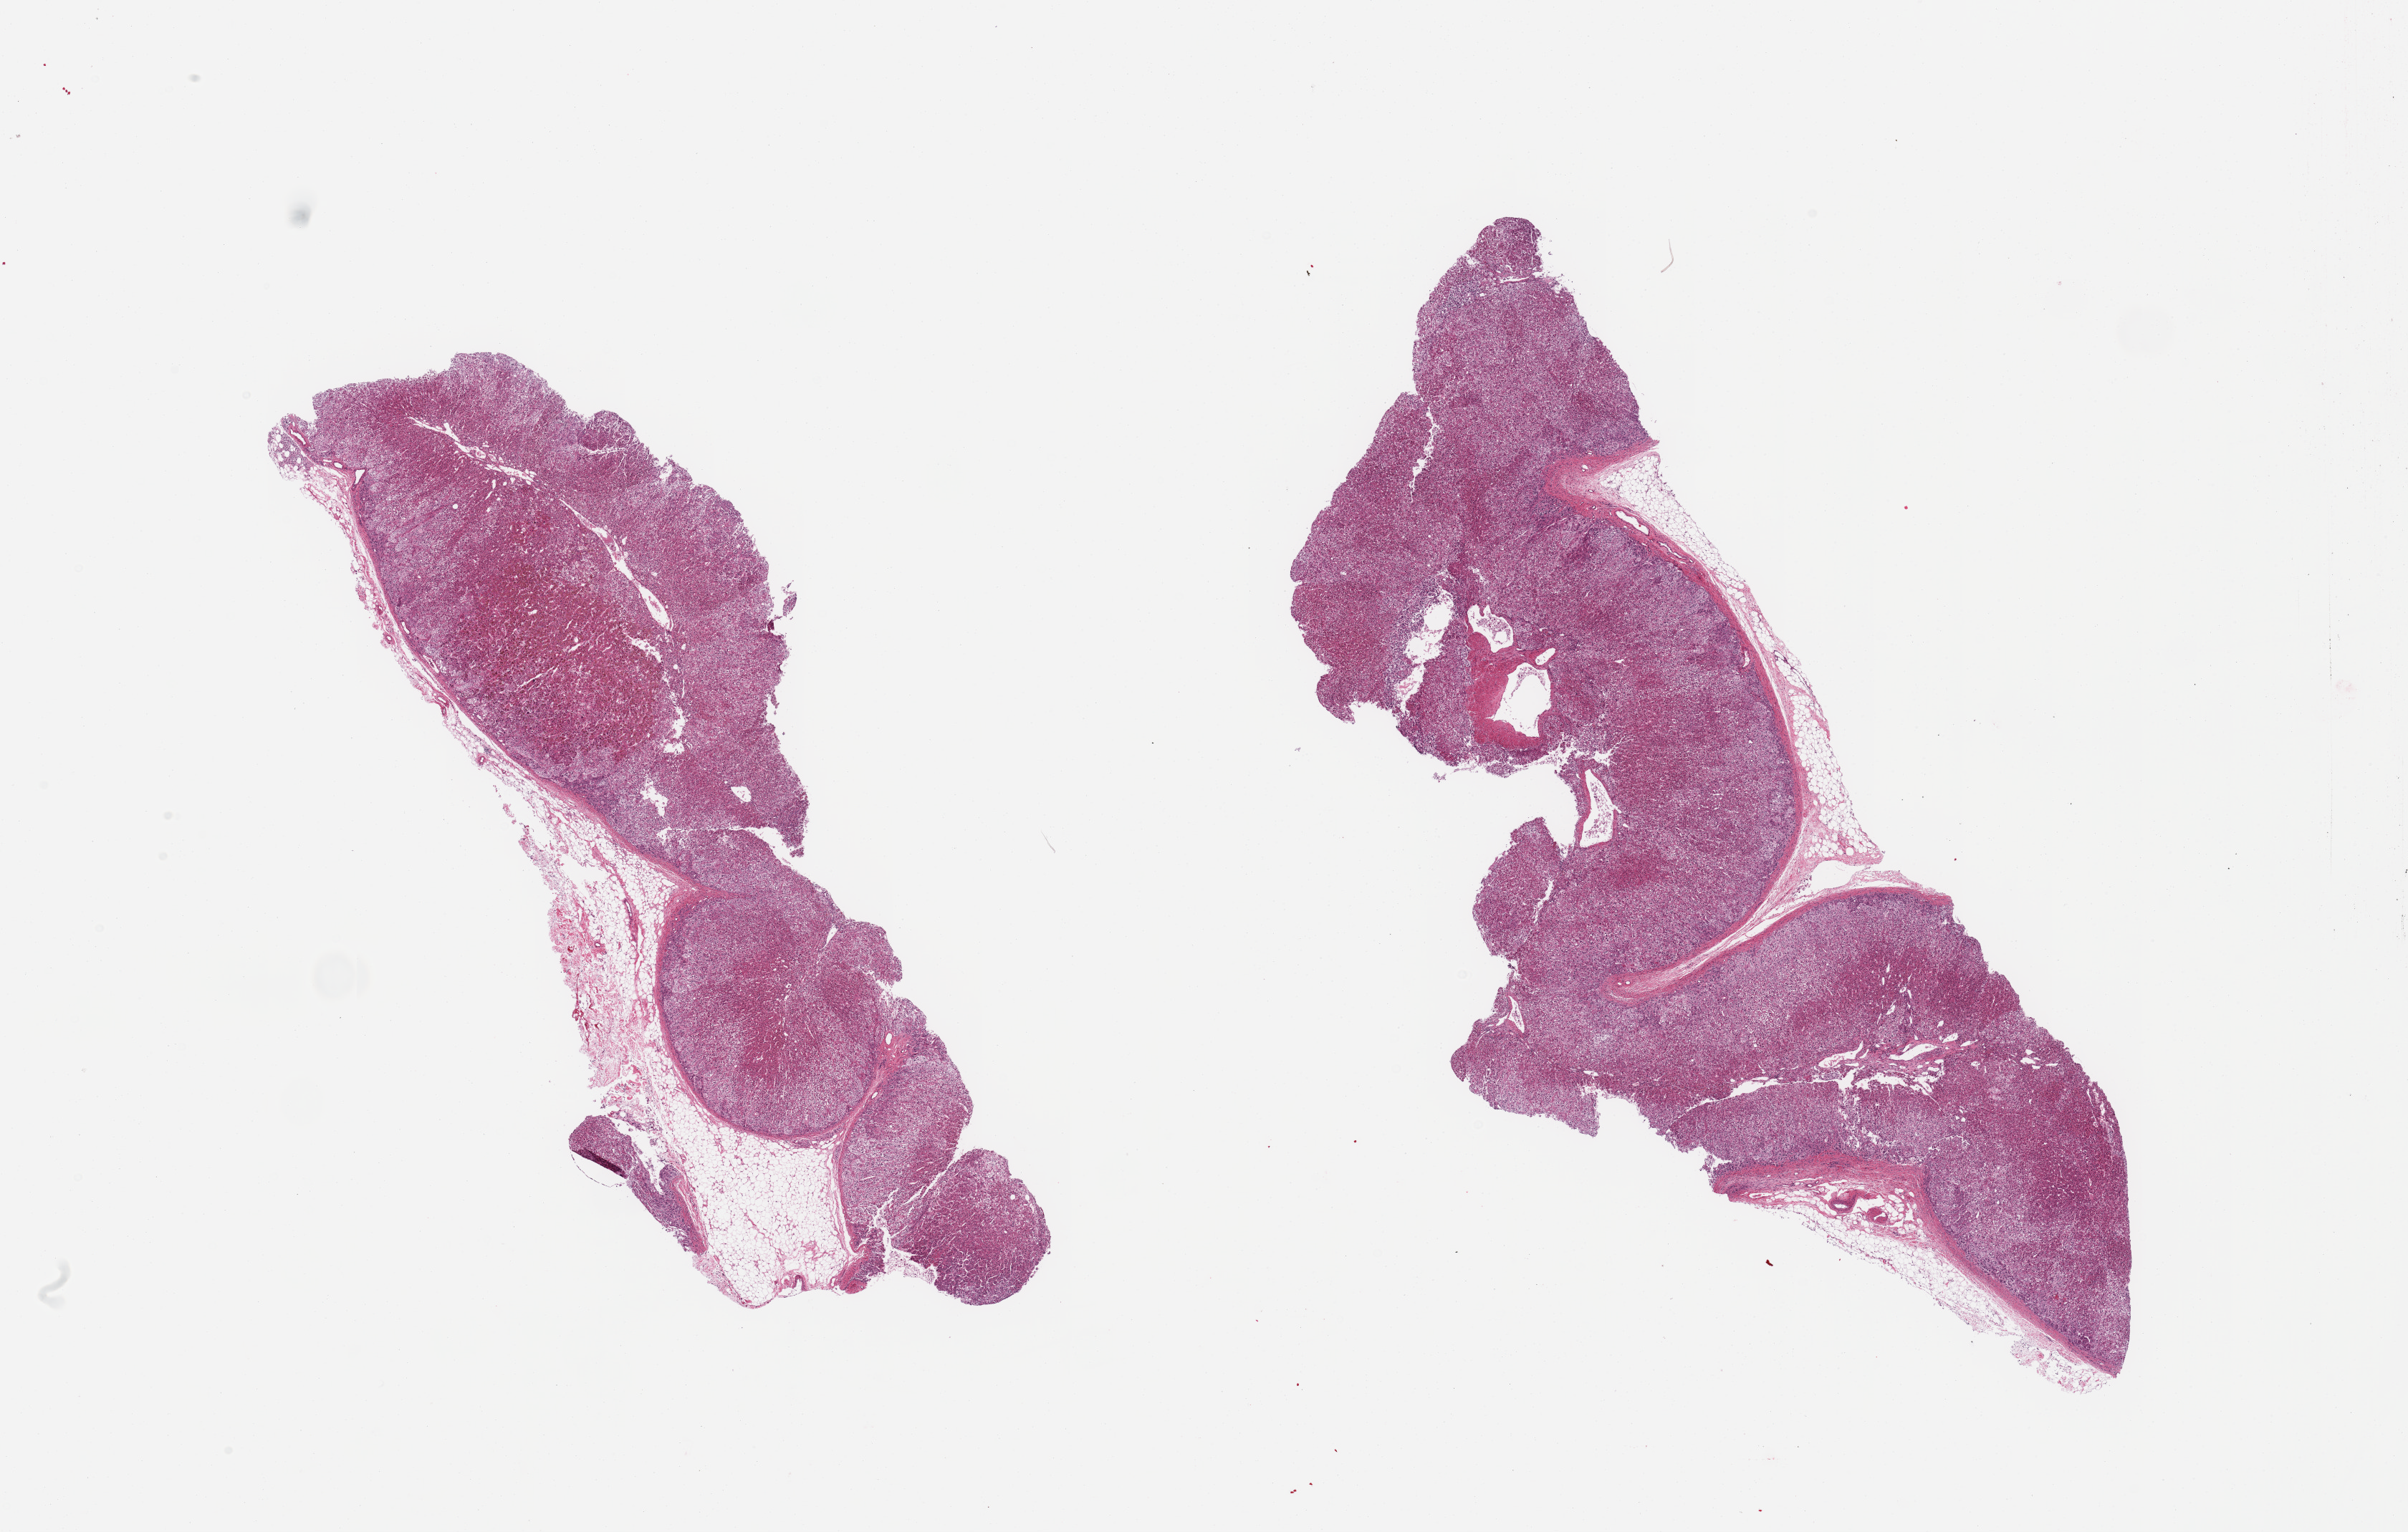
Digitized H&E-stained section, brightfield, whole scanned area (about 26.6 x 16.9 mm) shown as a low-resolution overview, PAXgene-fixed, paraffin-embedded tissue, section of adrenal gland (target tissue), donor tissue sample. Male donor.
- reviewer comment on this tissue sample: 2 pieces; adrenal cortex with attached 30% and 20% of external fat